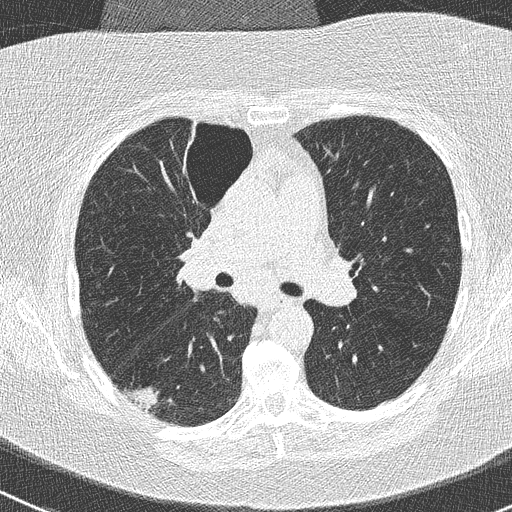
Chest CT (low-dose screening protocol), one axial image, first (baseline) screen, lung window (W 1500 / L -600 HU), 2 mm slice thickness, 512 × 512 image matrix, field of view 310 × 310 mm. Female participant, aged 74 years at enrolment. Former smoker at enrolment.
Expert reader's lesion annotation, bounding box (x1, y1, x2, y2) in pixels: (114, 378, 173, 424). The screening reader recorded 3 non-calcified nodules or masses ≥4 mm on this exam; which of them this box marks is not recorded. Official screen result: positive, change unspecified: nodule(s) >= 4 mm or enlarging nodule(s), mass(es), or other non-specific abnormalities suspicious for lung cancer.